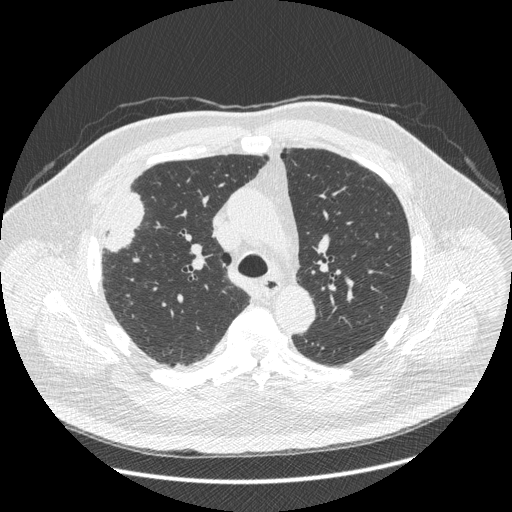
Low-dose screening chest CT, one axial slice; slice 293 of 426 in the series (ordered by position); 120 kVp; lung window (W 1500 / L -600 HU); 1.25 mm slice thickness; 512 × 512 image matrix.
Annotated regions visible in this slice (outlined manually by an expert reader):
- lesion 1 (tumor, upper lobe of right lung): bounding box <105,192,144,252> (left, top, right, bottom; pixels)